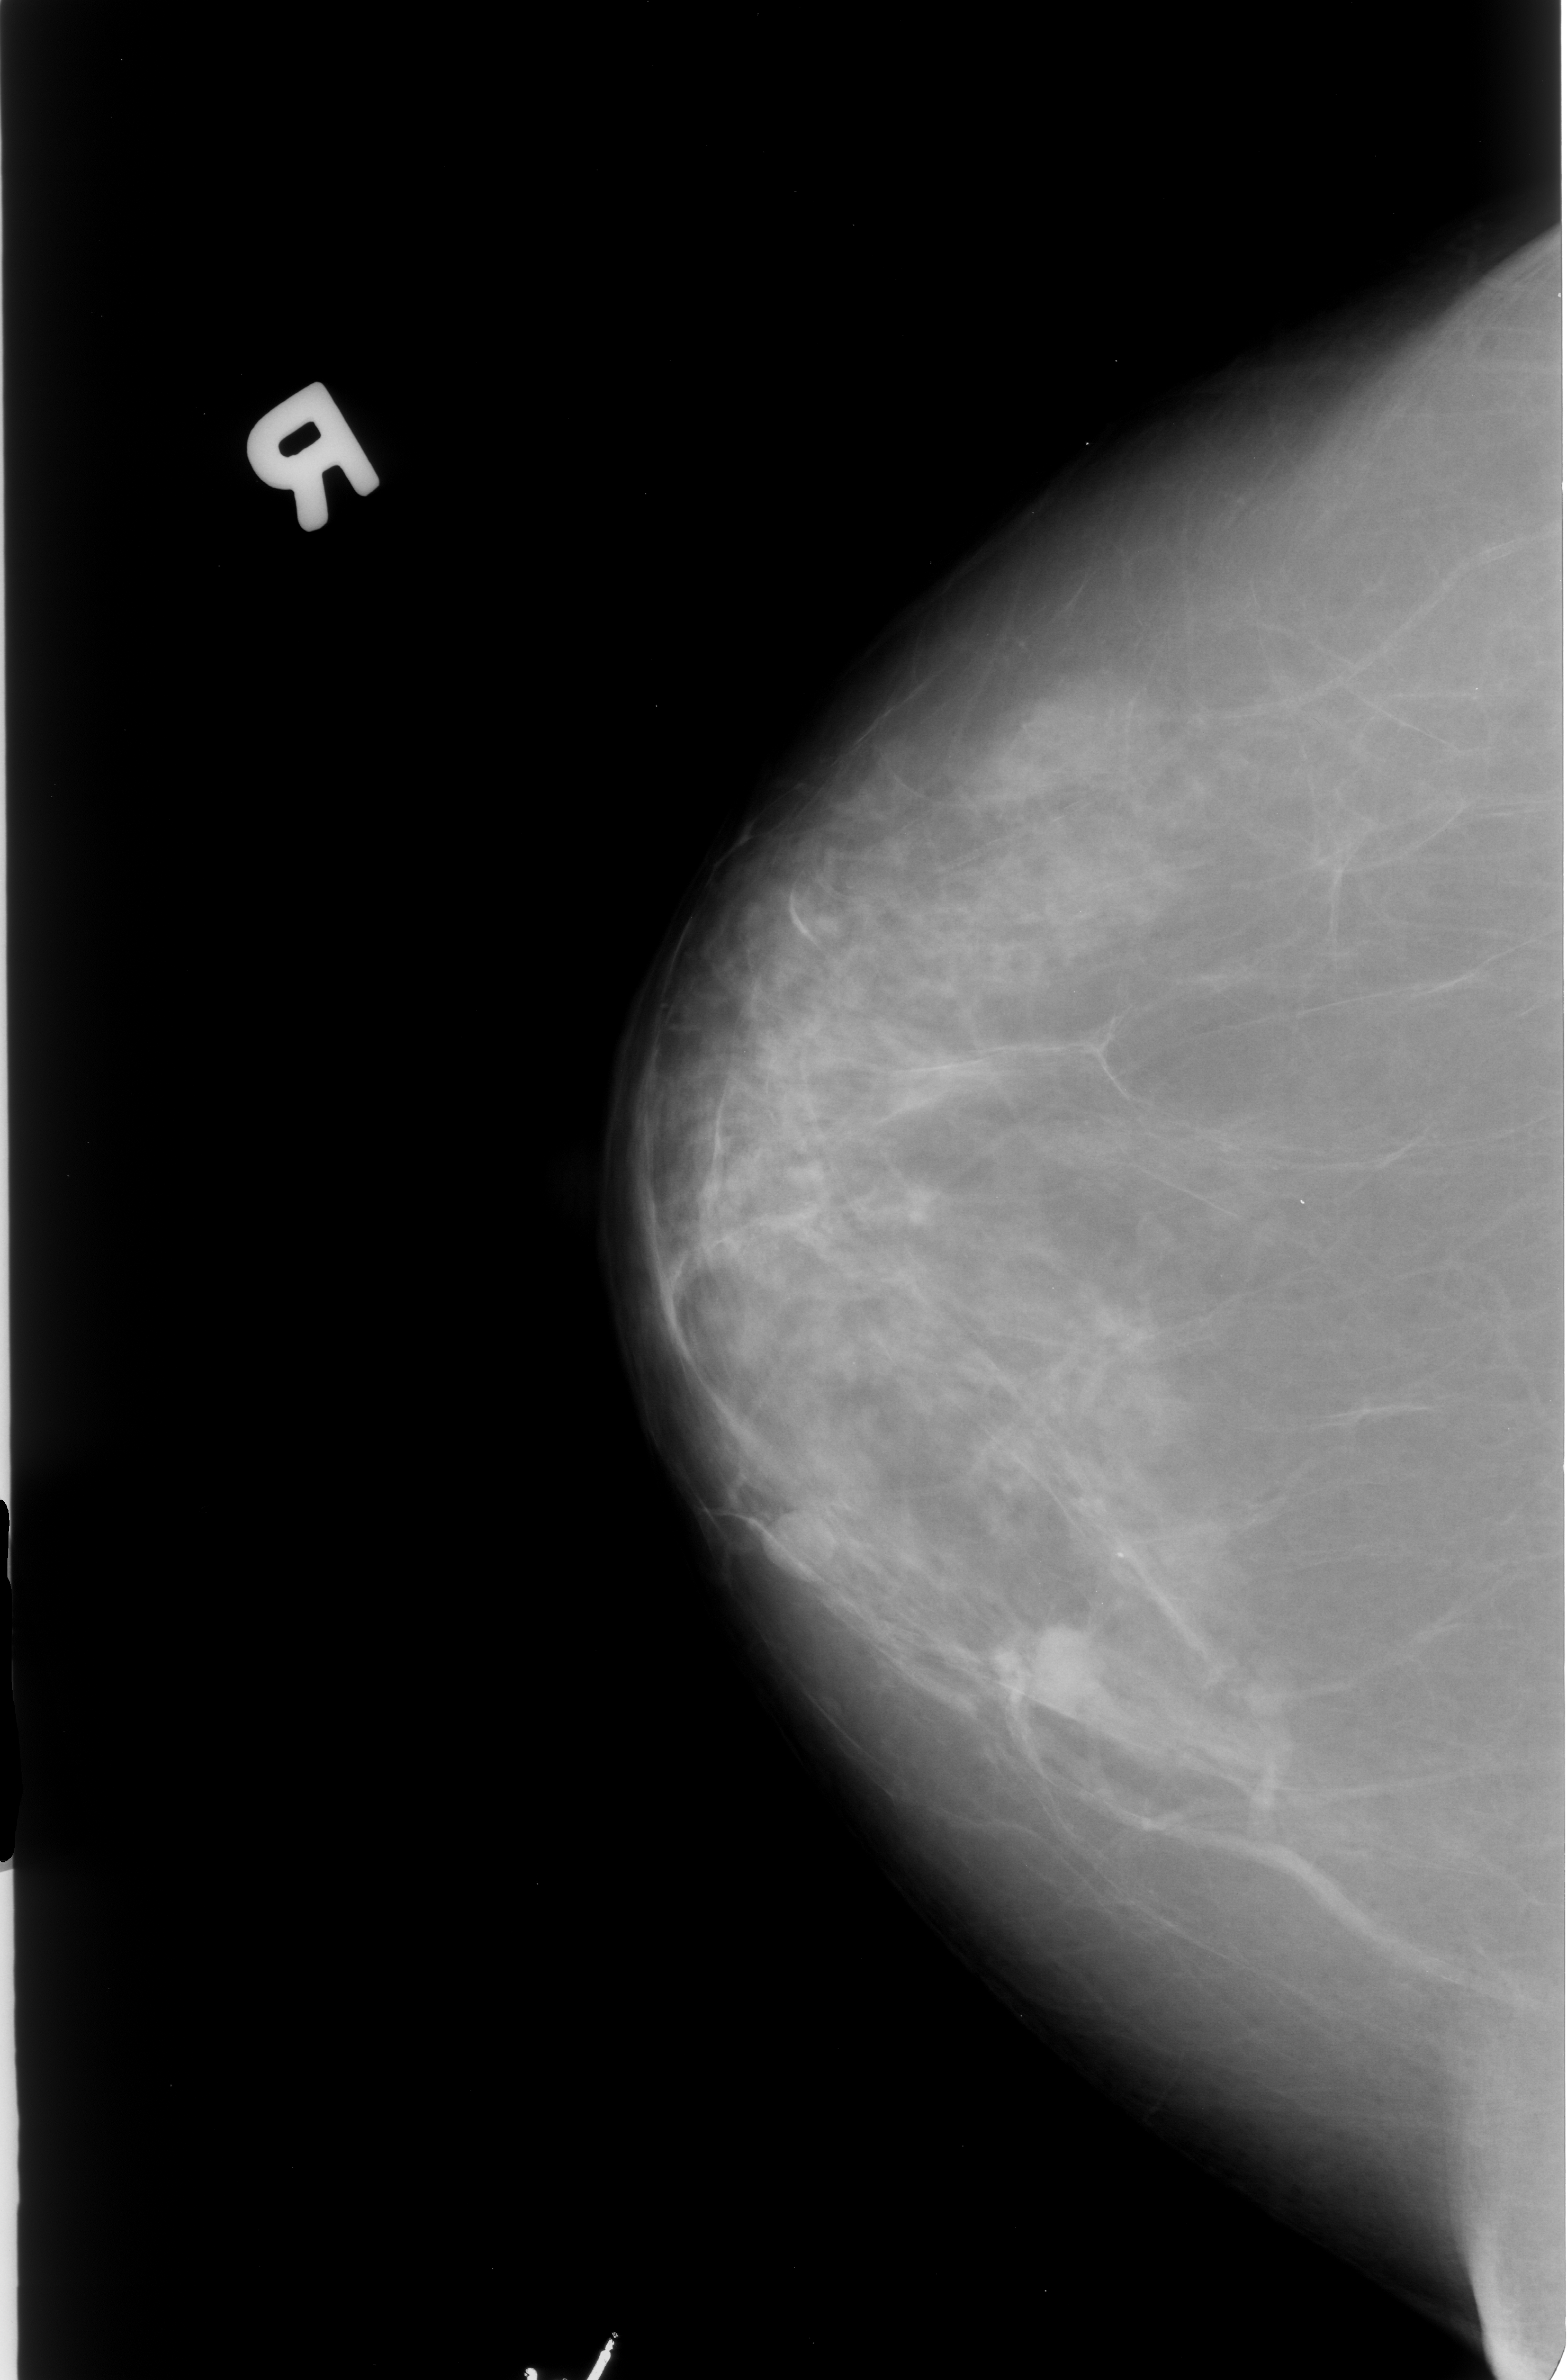
Digitized screen-film mammogram. Right breast. CC view. Breast composition: scattered fibroglandular densities (BI-RADS density category 2 of 4). 1567 × 2380 image matrix.
Expert-marked regions of interest on this image (one box per marked abnormality):
- mass, shape irregular / architectural distortion, margins microlobulated / ill defined / spiculated; BI-RADS assessment category 4; subtlety rating 4 on a 1 (subtle) to 5 (obvious) scale; pathology result (as recorded, not read from the image): malignant: bounding box (x1, y1, x2, y2) in pixels: (980, 1614, 1104, 1724)